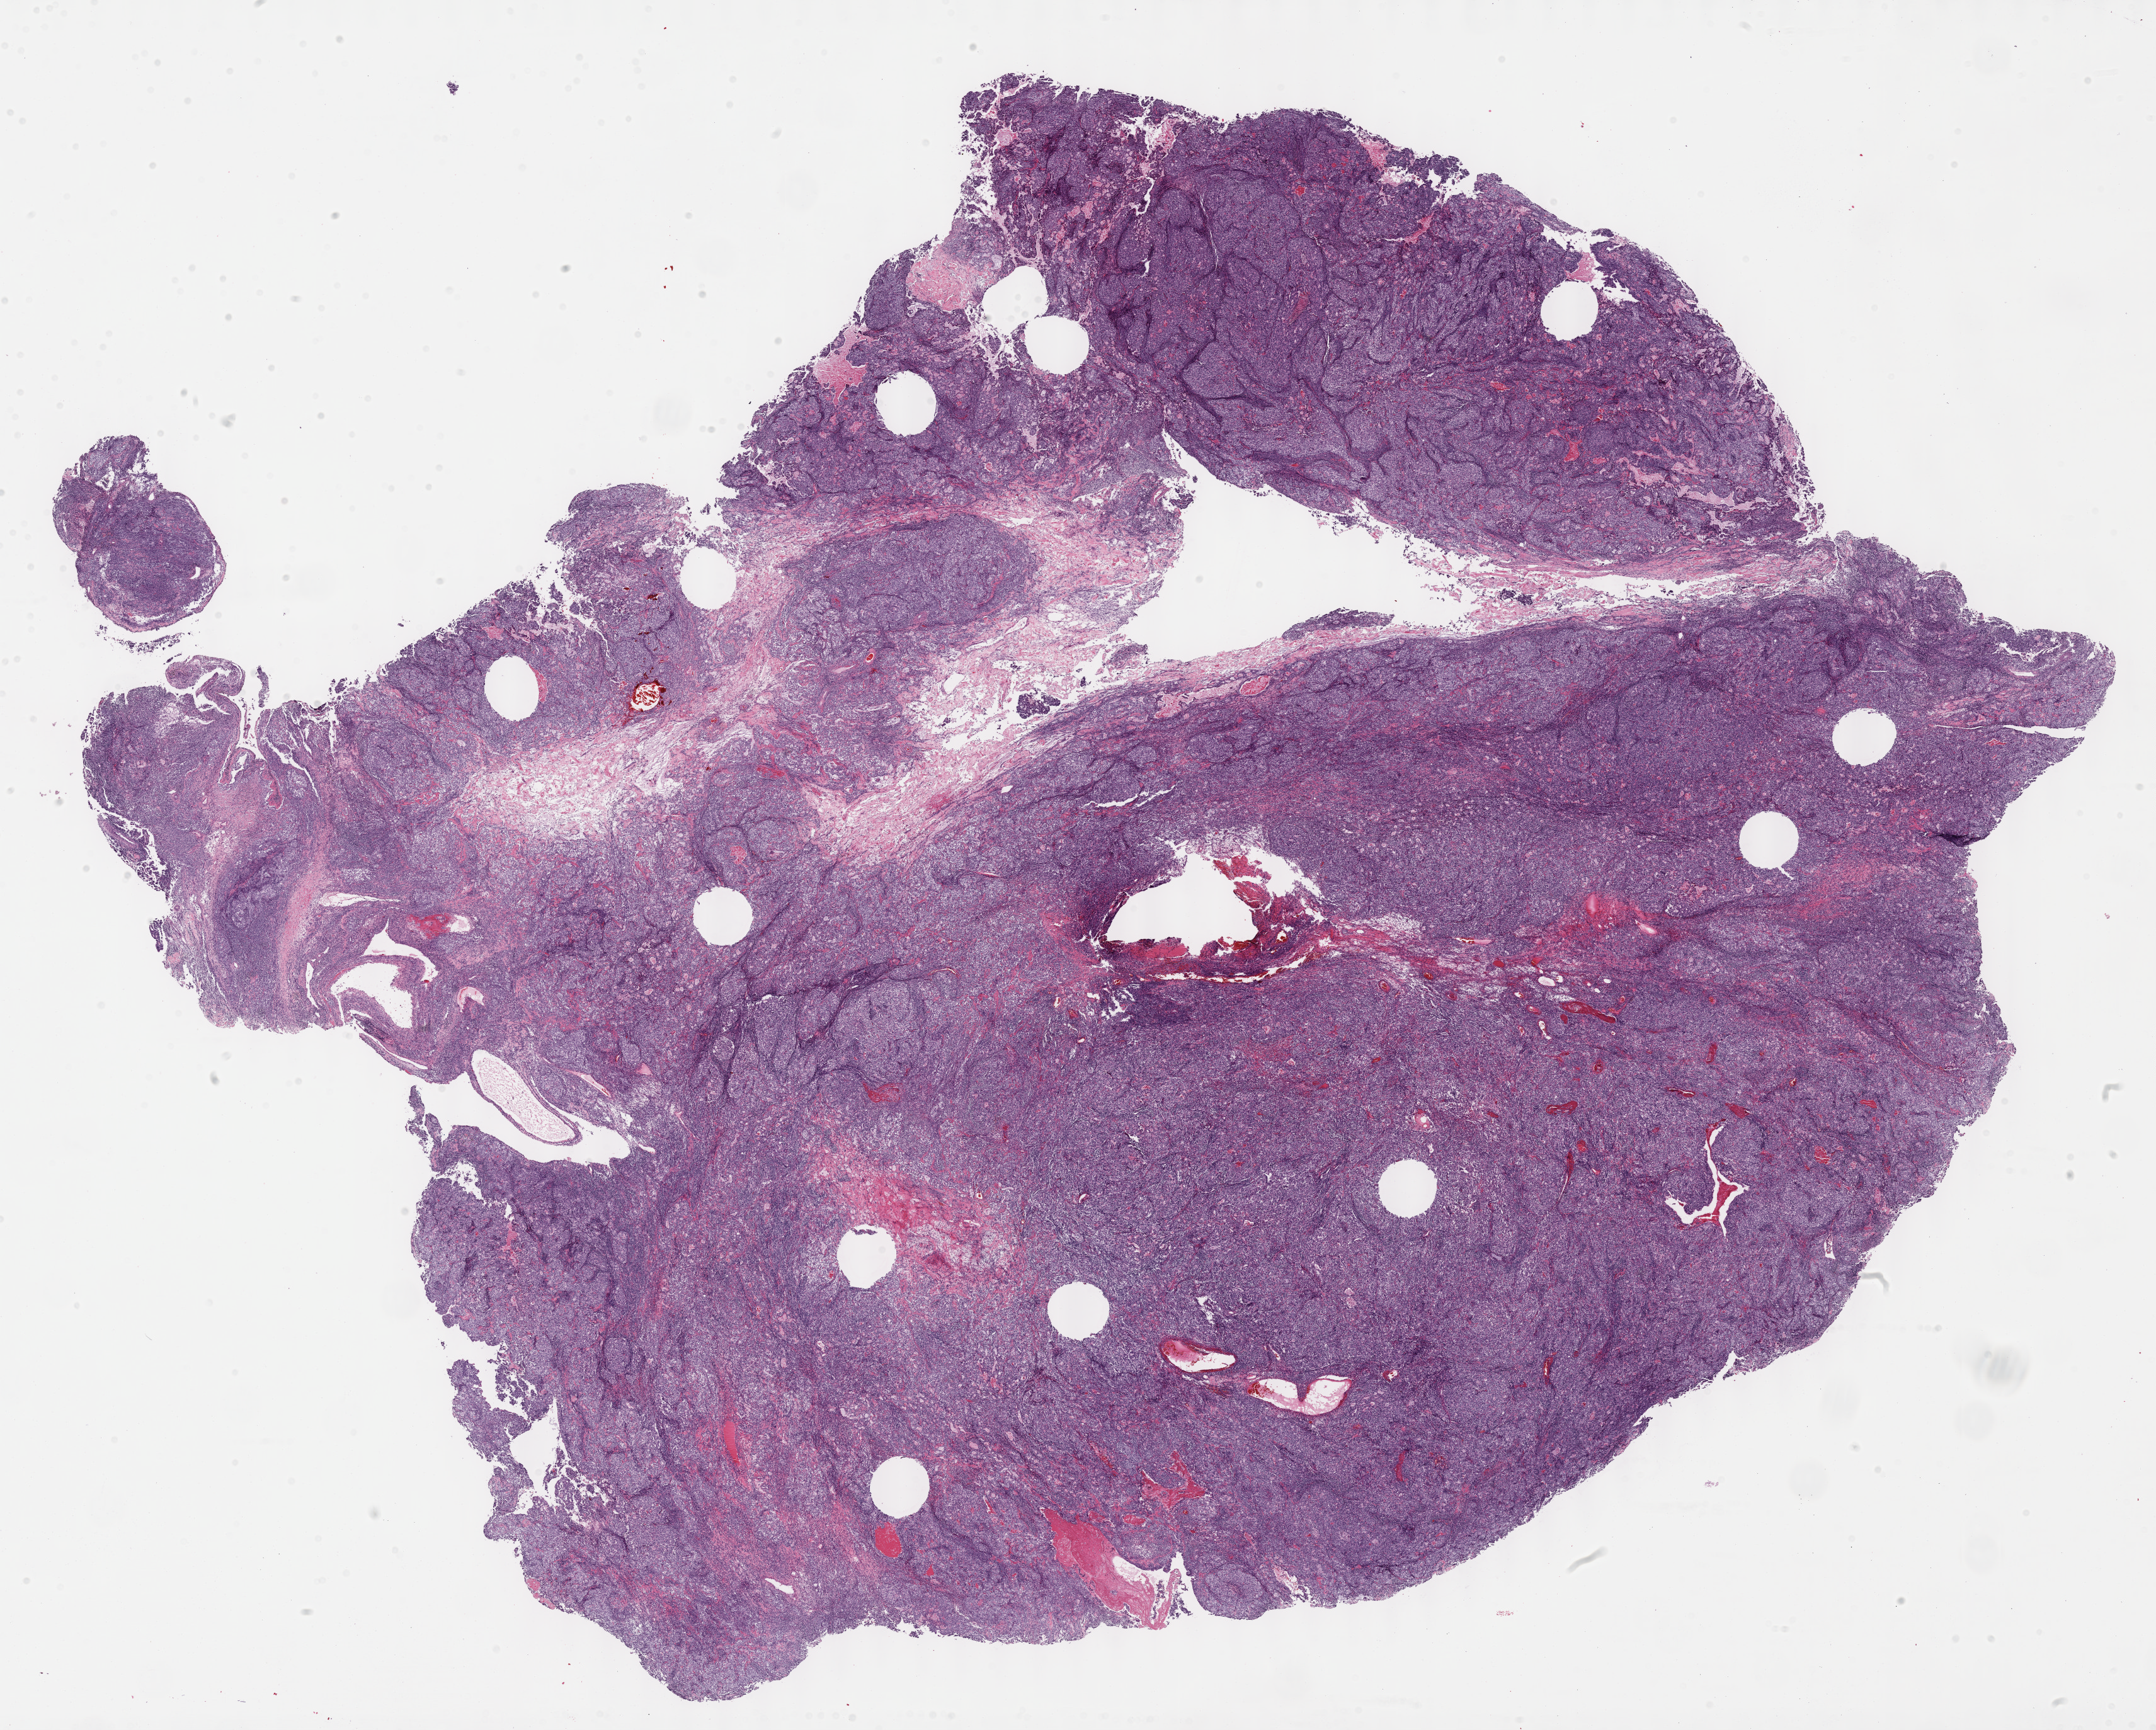
H&E whole-slide image, whole scanned area (about 27.7 x 22.2 mm) shown as a low-resolution overview, formalin-fixed paraffin-embedded (FFPE) diagnostic section, sample: primary tumour, connective, subcutaneous and other soft tissues. Patient: female, age at initial diagnosis 20 years.
Histologic diagnosis: Synovial sarcoma, biphasic (connective, subcutaneous and other soft tissues of trunk, NOS).